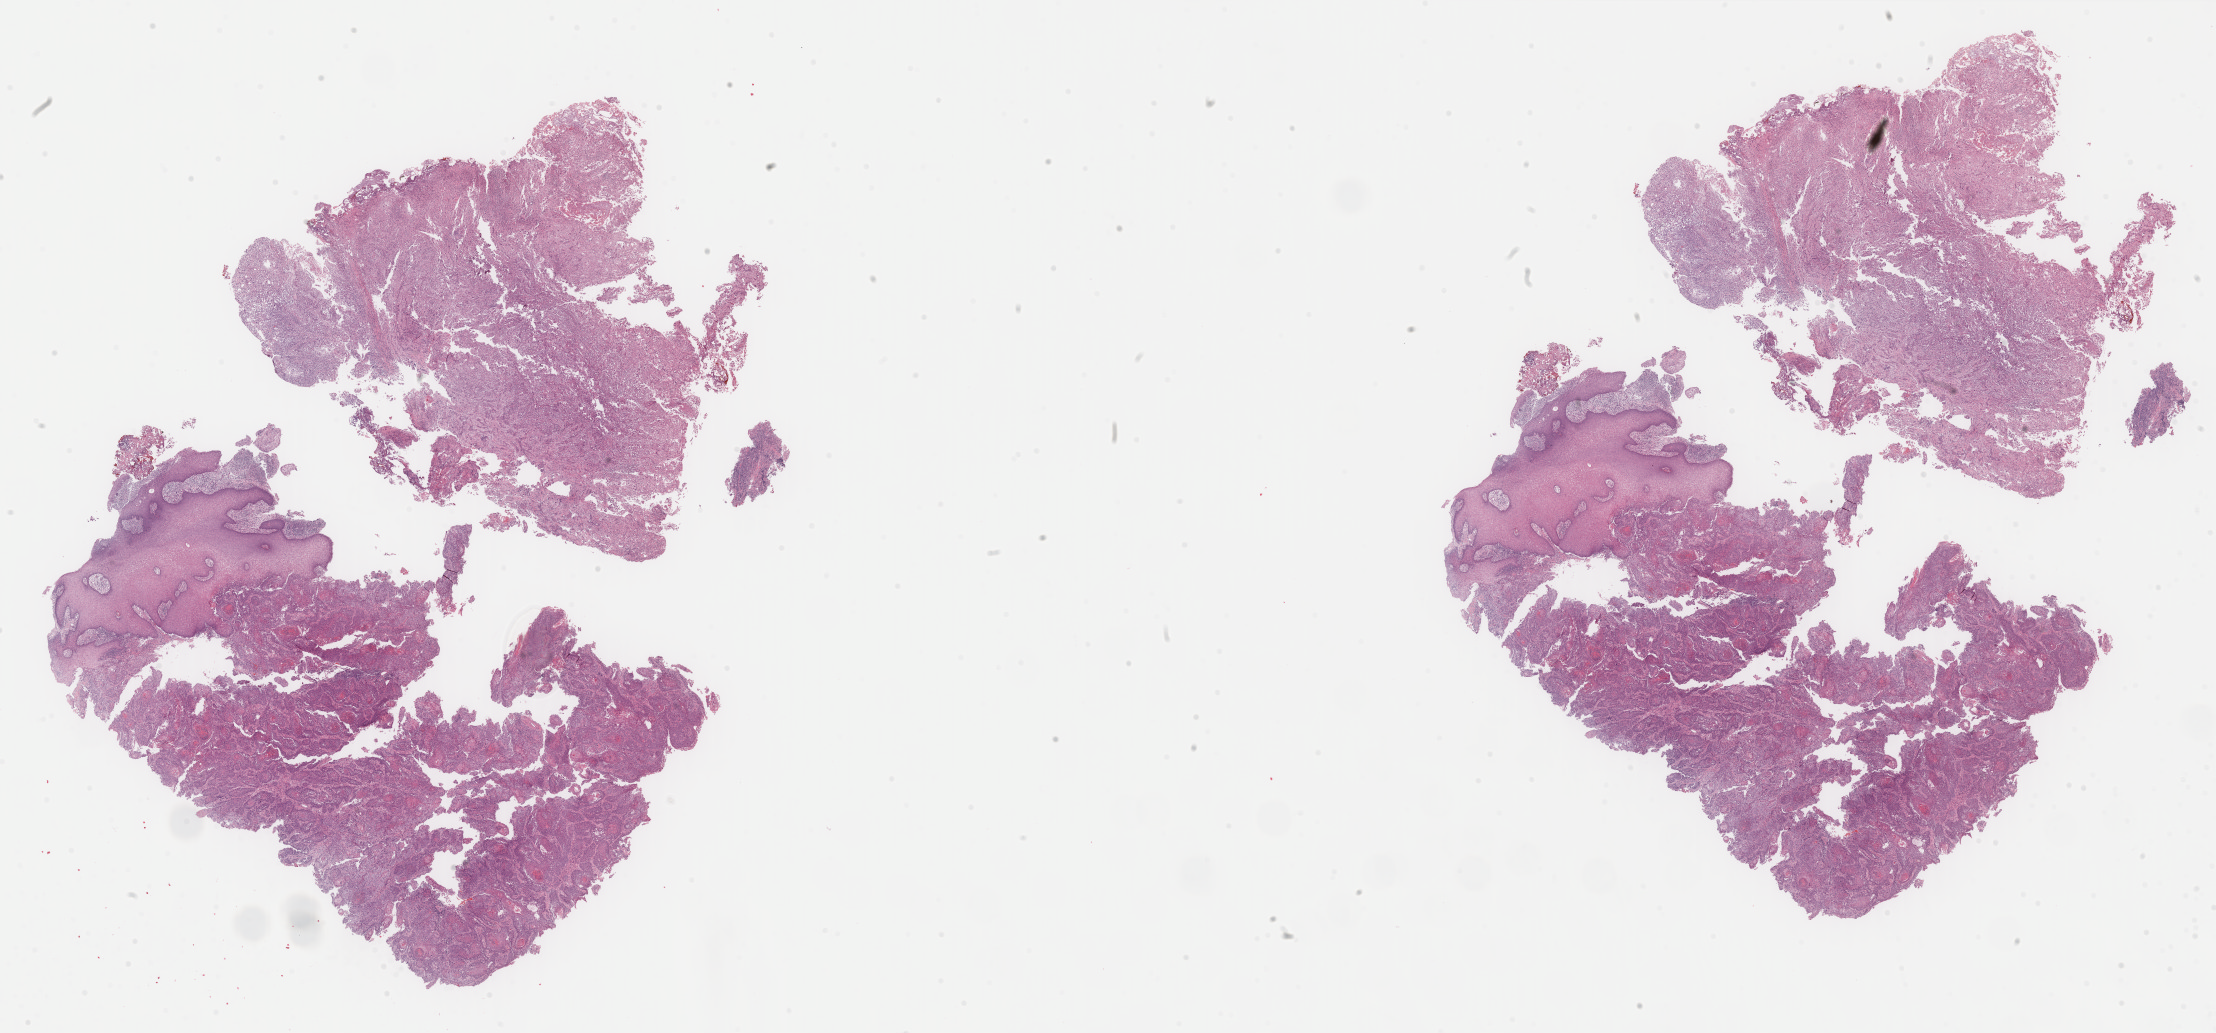
Whole-slide histology image, H&E-stained — shown as a low-resolution overview of the whole scanned area (about 35.1 x 16.3 mm, slide scanned at 40x). Formalin-fixed paraffin-embedded (FFPE) diagnostic section. Primary tumour sample from the head and neck. Male patient; age at initial diagnosis 59 years. Histologic grade: G2 (moderately differentiated).
Laterality: right. Diagnosis: Squamous cell carcinoma, NOS (oropharynx, NOS).